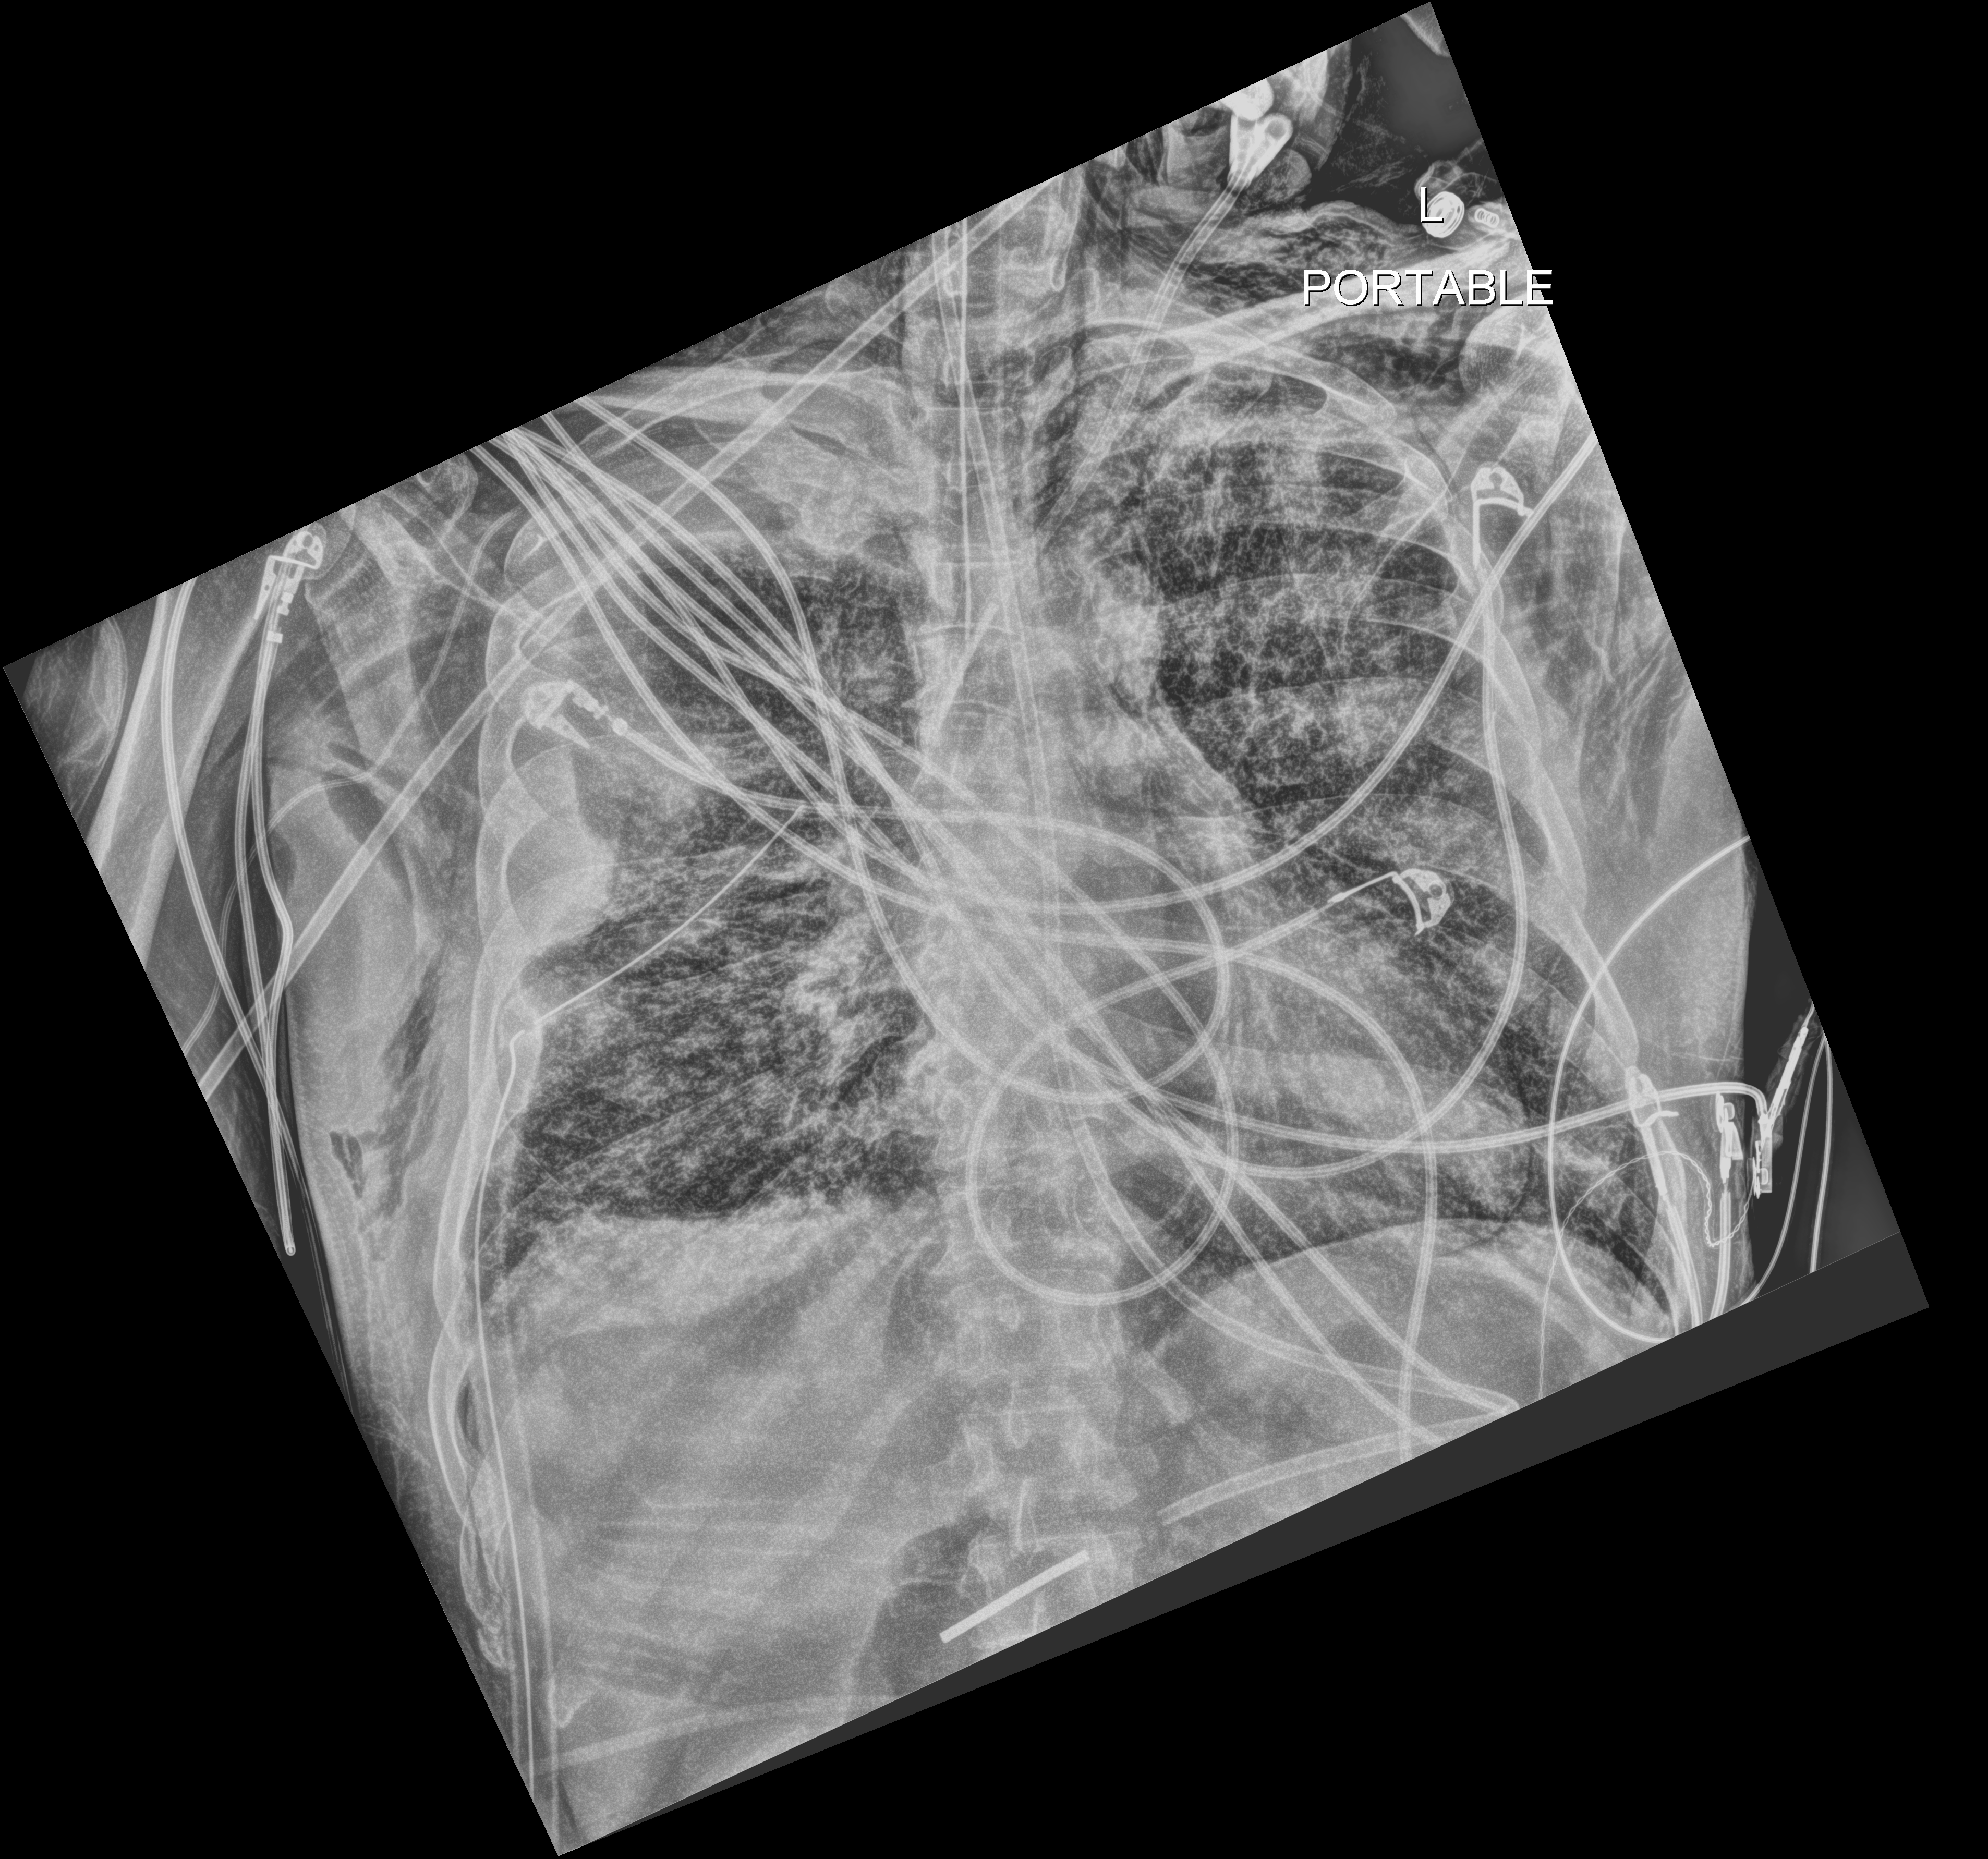
Portable chest radiograph; anteroposterior (AP) projection. Patient hospitalised with COVID-19; male, aged 18–59 years.
Admission-level facts for this patient (not findings on this image; timing relative to this image not recorded): COPD (admission record): no; admitted to intensive care during this hospital stay: yes; mechanically ventilated during this hospital stay: yes.